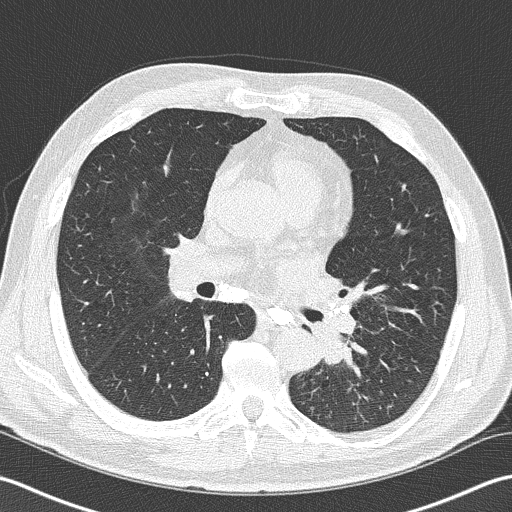
Low-dose screening chest CT, axial slice; second screening round (one year after baseline); lung window (W 1500 / L -600 HU); 2 mm slice thickness; slice 76 of 170 in the series. Male participant, aged 57 years at enrolment.
Expert reader's lesion annotation, box from (x=293, y=300) to (x=373, y=380) px. The exam's reader record, not a measurement of the box and not confirmed to be the same lesion: non-calcified nodule or mass ≥4 mm, left lower lobe, 40 × 30 mm, spiculated (stellate) margins, soft tissue attenuation, pre-existing on the prior screen: no. Lung cancer was diagnosed 9 days after this screen: squamous cell carcinoma, NOS, left lower lobe, moderately differentiated (G2), stage IIIB (AJCC 6th edition), 38 mm at pathology.